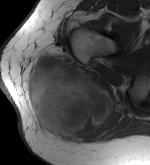
MRI of an extremity soft-tissue mass, one axial slice. Slice 30 of 56 in the series (ordered by position). MR volume resampled by the dataset authors to the PET/CT grid (not the native acquisition matrix). 3.27 mm slice thickness. 150 × 165 image matrix, field of view 146 × 161 mm. Female patient. Case-level facts recorded for this patient, not image findings: histological type: epithelioid sarcoma with vascular differentiation; site of the primary tumour: right buttock.
Structures marked on this image (expert contour drawn on MRI and transferred to this co-registered scan by the dataset authors):
- gross tumour volume (mass): bounding box (x1, y1, x2, y2) in pixels: (25, 51, 115, 137)